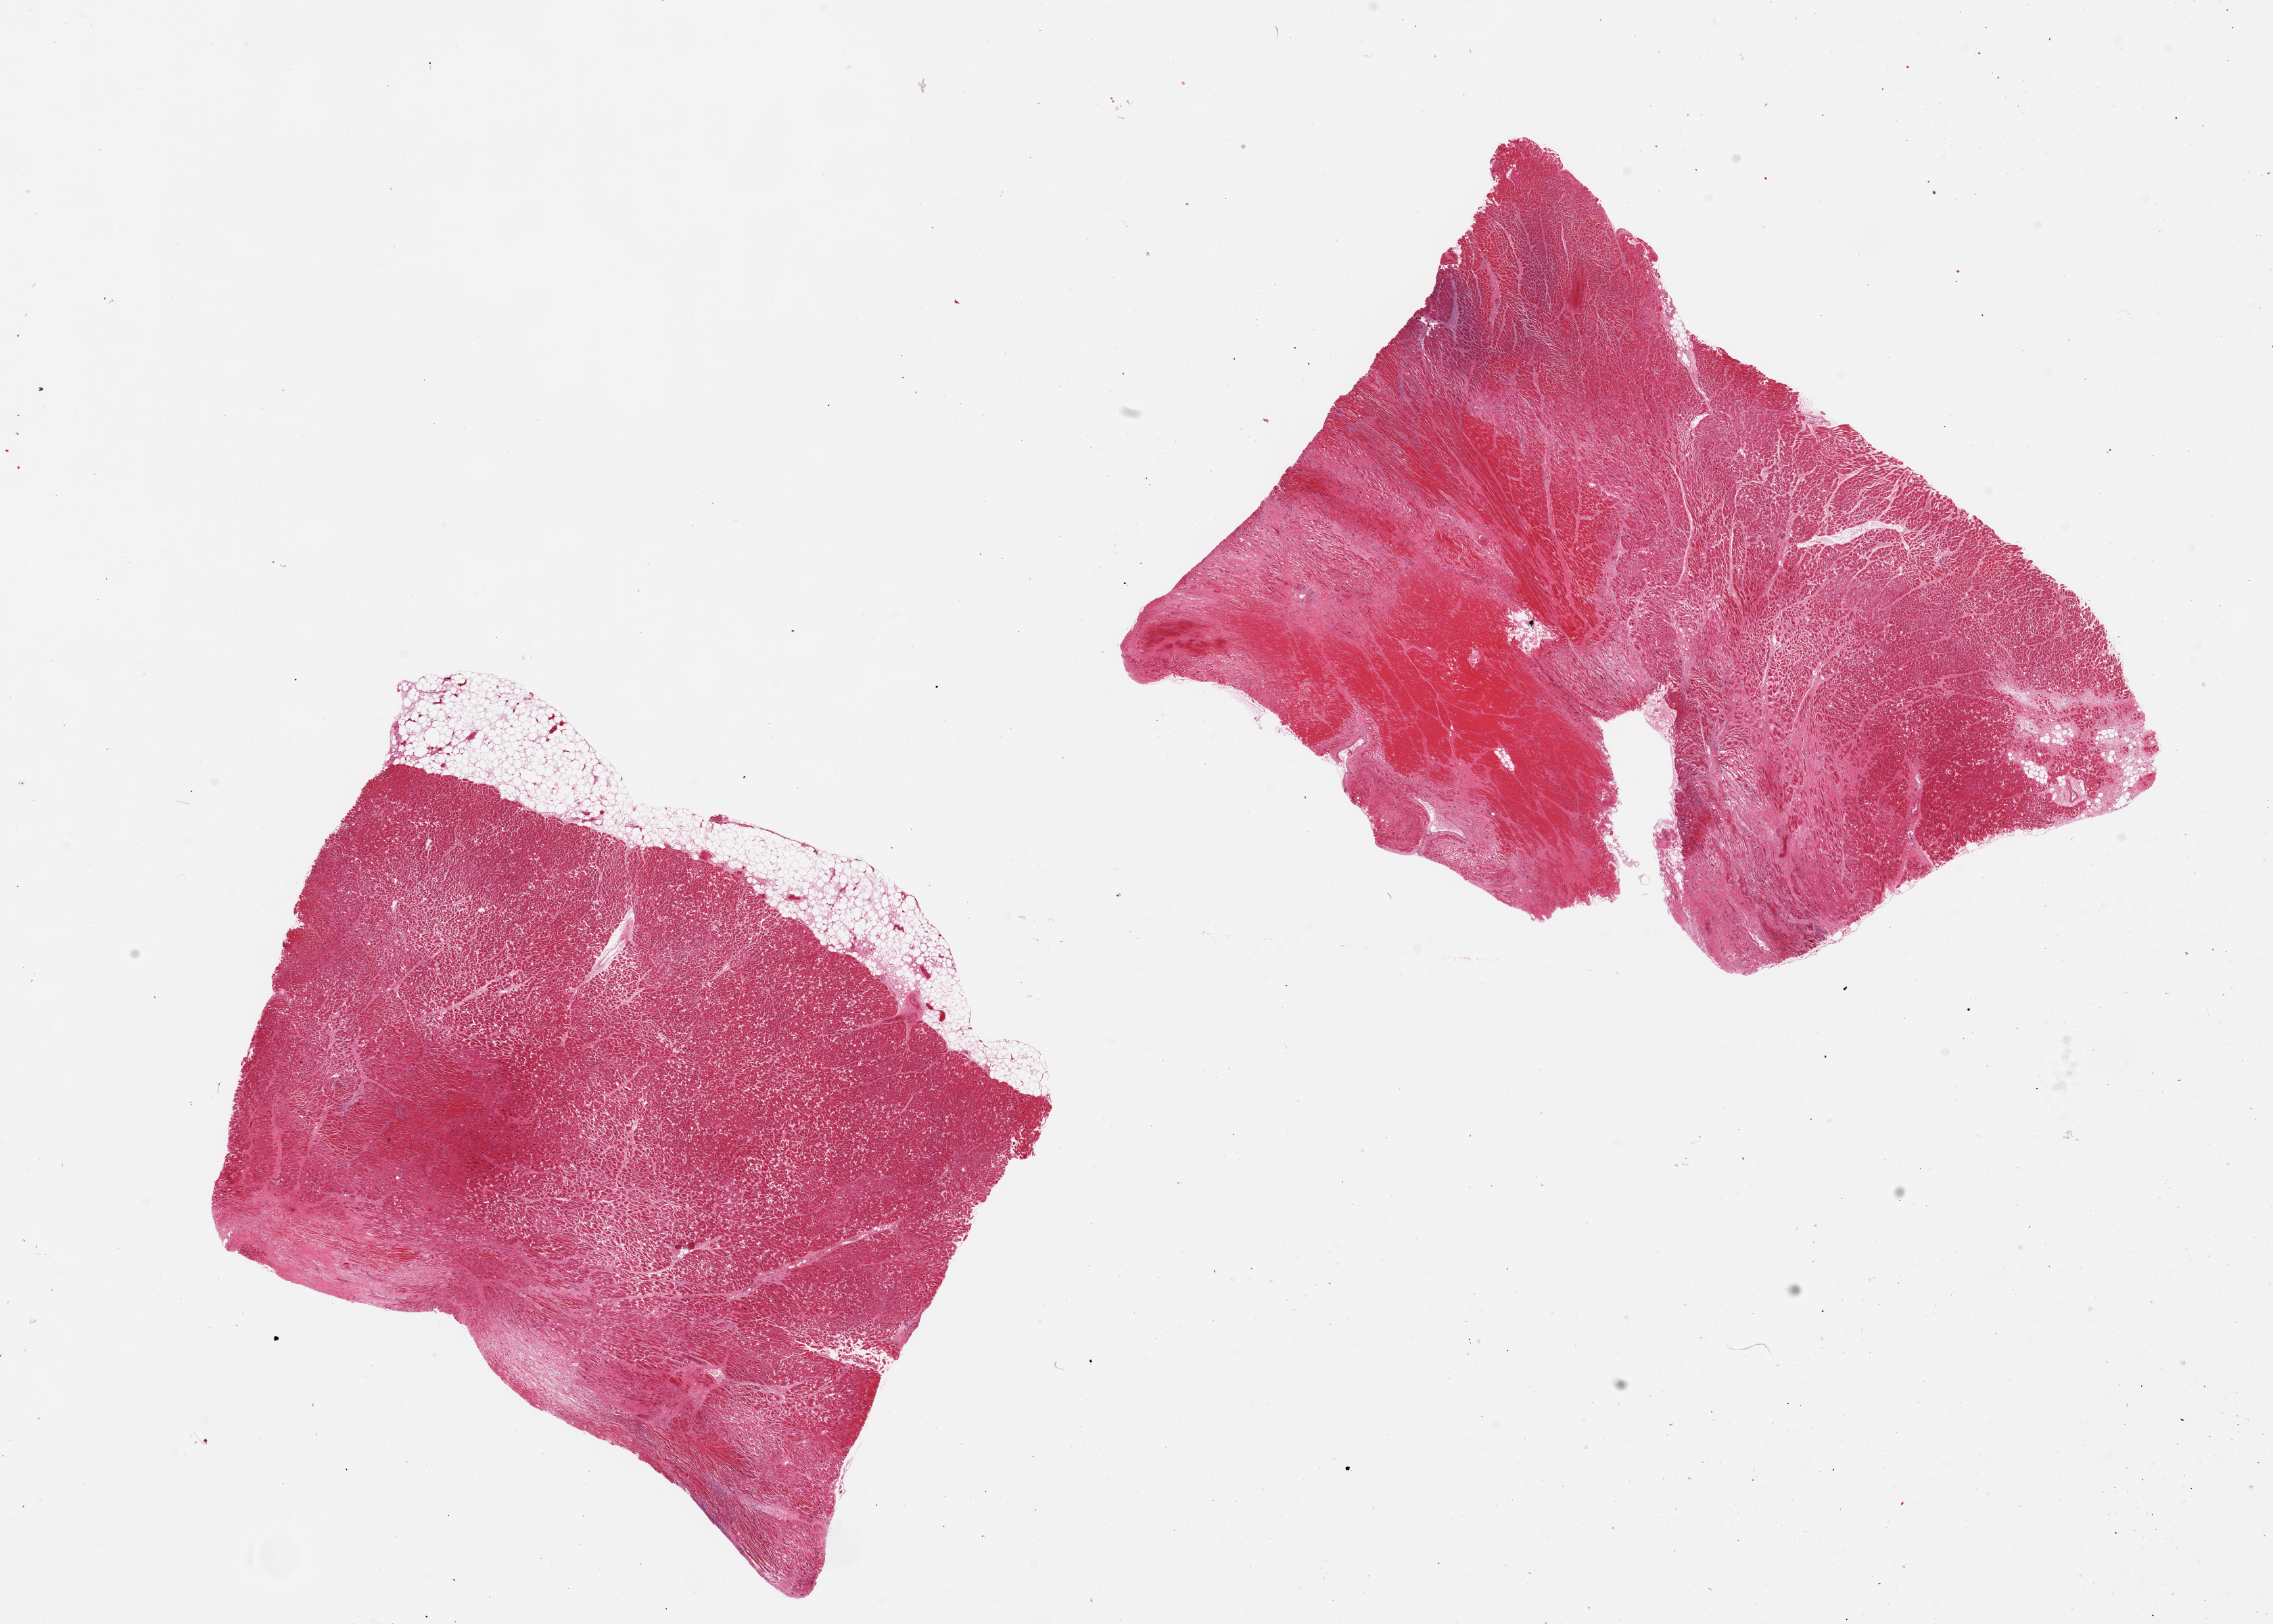
Whole-slide image, H&E stain, a low-resolution overview of the entire scanned area, about 26.6 x 19.0 mm, PAXgene-fixed, paraffin-embedded tissue, sampled site (target tissue): heart, donor tissue sample. Donor: female.
* reviewer comment on this tissue sample: 2 pieces, evidence of remote (fibrosis) and acute myocardial infarction (coagulative necrosis, edema, neutorphilic infiltrate)